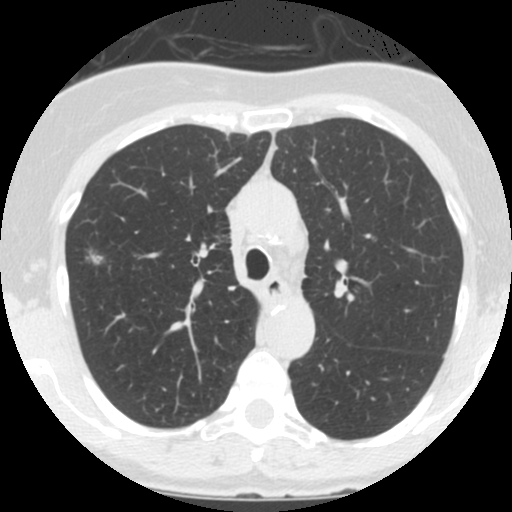
Low-dose screening chest CT, one axial slice; position 102 of 146 along the scan axis; lung window (W 1500 / L -600 HU); 2.5 mm slice thickness; 512 × 512 image matrix.
Annotated regions visible in this slice (expert manual segmentation):
- lesion 1 (tumor, upper lobe of right lung): bounding box (x1, y1, x2, y2) in pixels: (84, 247, 106, 266)